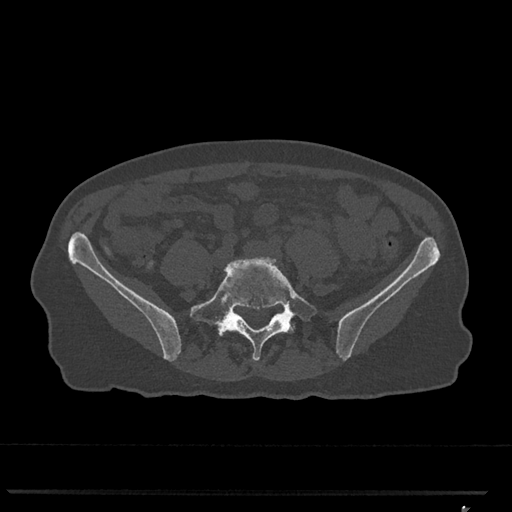
CT including the spine, one axial slice. Slice 153 of 793 in the series (ordered by position). 120 kVp. Bone window (W 1800 / L 400 HU). 512 × 512 image matrix, field of view 380 × 380 mm. Patient: female, 62 years. From the clinical record (not read from this slice): primary cancer: renal.
Annotated regions visible in this slice (semi-automatically segmented with operator editing):
- L5 vertebra: box from (x=190, y=257) to (x=316, y=361) px